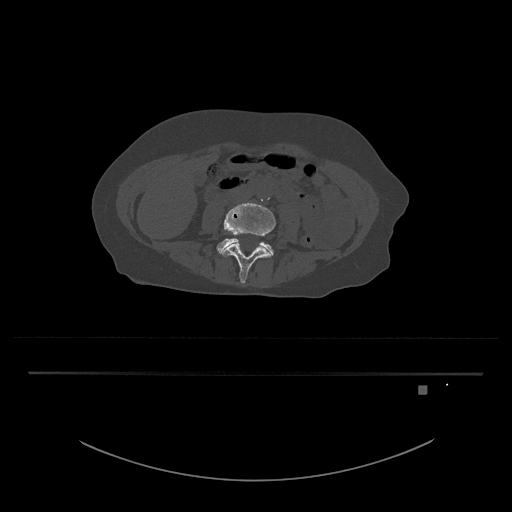
CT including the spine, one axial slice; position 346 of 797 along the scan axis; reconstruction kernel Br40s/3; bone window (W 1800 / L 400 HU); 512 × 512 image matrix, field of view 500 × 500 mm. Female patient, age 57 years. From the clinical record (not read from this slice): primary cancer: cervical.
Structures marked on this image (semi-automatically segmented with operator editing):
- L4 vertebra: bounding box (x1, y1, x2, y2) in pixels: (220, 203, 276, 283)